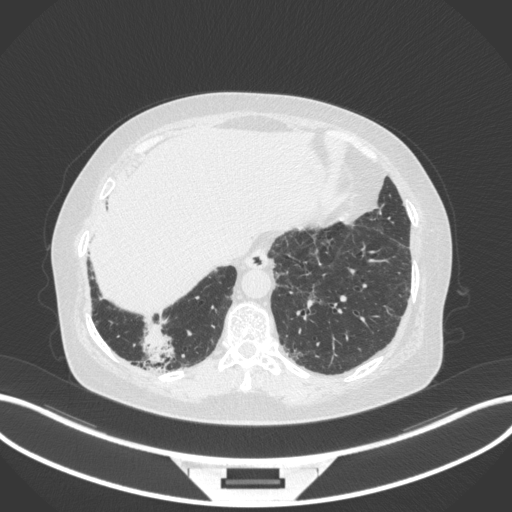
Chest CT, one axial slice. Position 27 of 303 along the scan axis. 120 kVp. Lung window (W 1500 / L -600 HU). 1 mm slice thickness. 512 × 512 image matrix. Female patient, age 65 years. Case-level facts recorded for this patient, not image findings: clinical TNM (as recorded): T2b N1 M0; histopathological grade: G1.
Structures marked on this image (rectangle marked by the reading radiologist):
- lung tumour (recorded histology: adenocarcinoma): bounding box (x1, y1, x2, y2) in pixels: (139, 322, 176, 368)